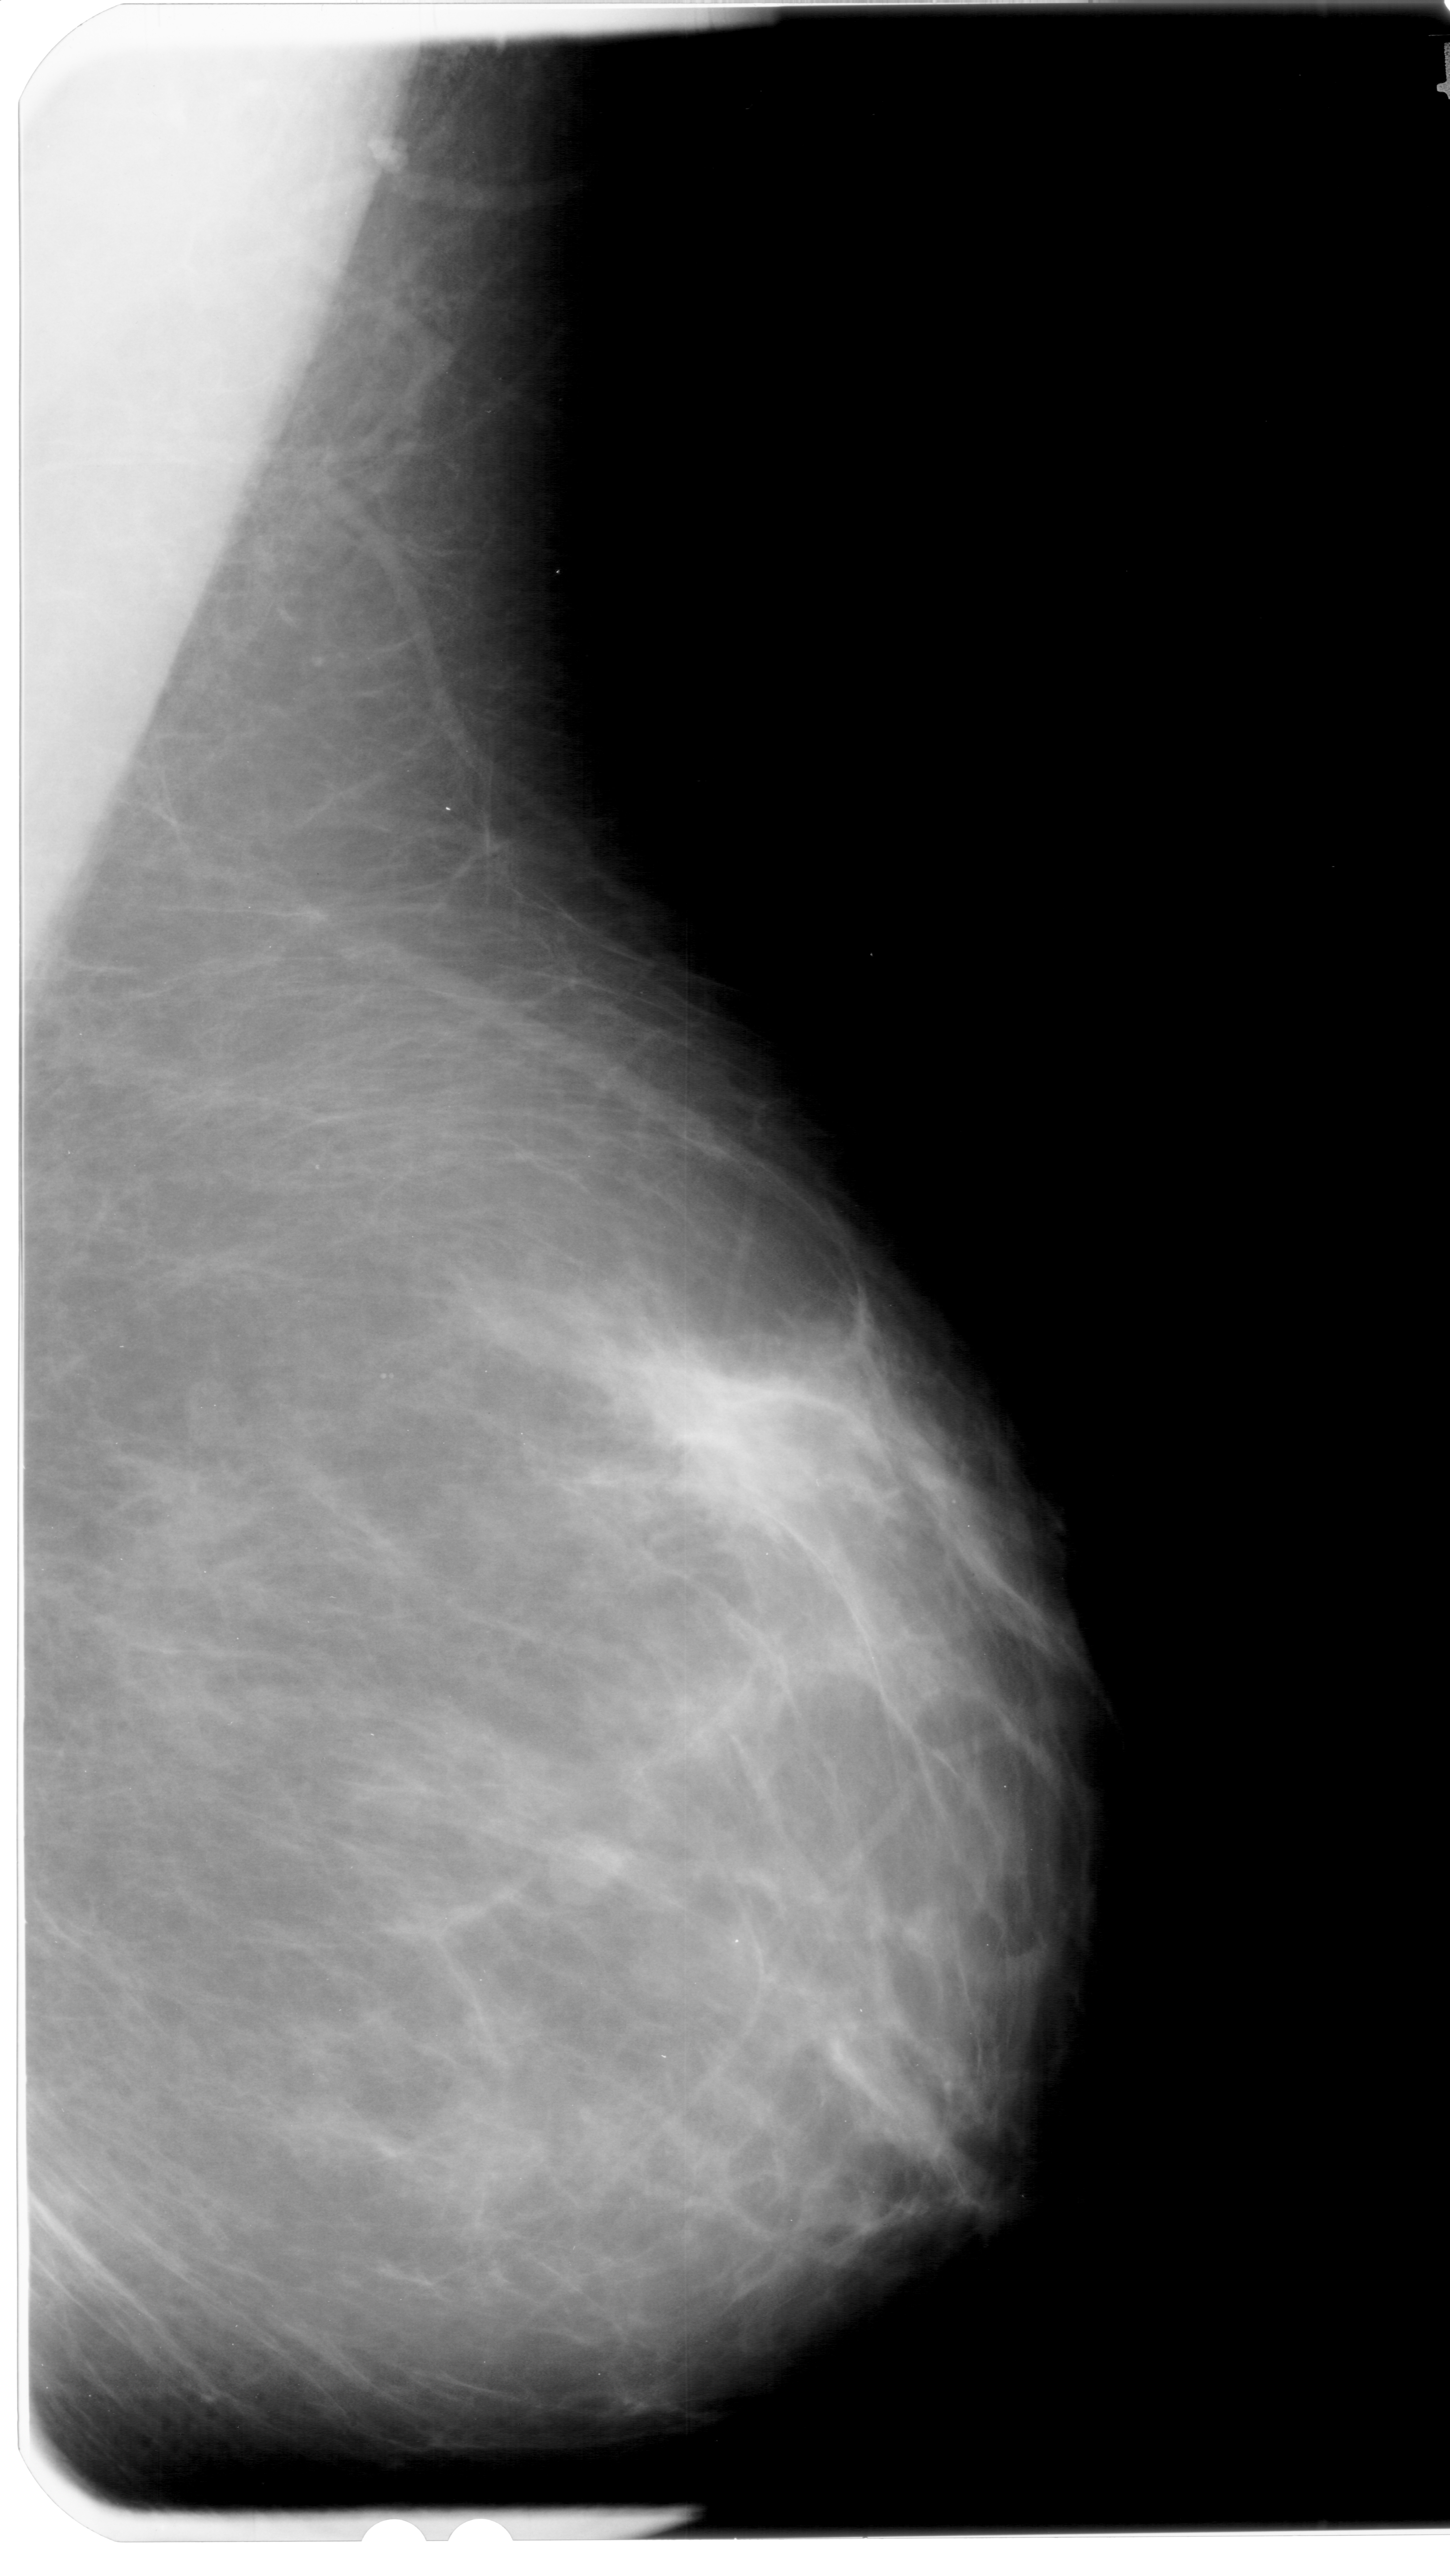
Scanned film-screen mammogram. Right breast. Mediolateral oblique (MLO) view. BI-RADS breast density category 2 (scale 1–4). 1450 × 2576 image matrix.
Expert-marked regions of interest on this film, with their recorded descriptors:
- mass, shape round, margins circumscribed; BI-RADS assessment category 3; pathology result (as recorded, not read from the image): benign: box from (x=557, y=1828) to (x=652, y=1902) px